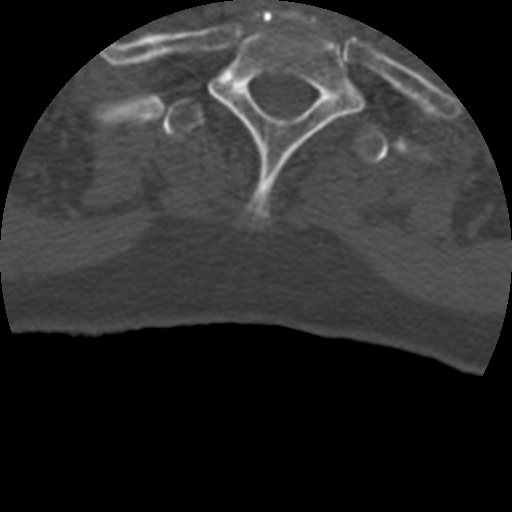
CT including the spine, one axial slice. Slice 382 of 399 in the series (ordered by position). Reconstruction kernel STANDARD. Bone window (W 1800 / L 400 HU). 1.25 mm slice thickness. 512 × 512 image matrix. Patient age 69 years. Case-level facts recorded for this patient, not image findings: primary cancer: prostate.
Annotated regions visible in this slice (semi-automatically segmented with operator editing):
- T1 vertebra: bounding box (x1, y1, x2, y2) in pixels: (209, 17, 364, 222)
- T2 vertebra: (162, 96, 389, 164)